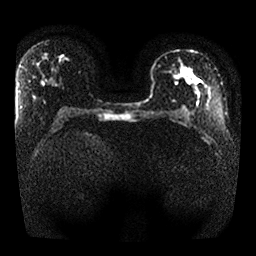
Breast MRI, one axial slice. Slice 13 of 25 in the series (ordered by position). Diffusion-weighted series; image 2 of 4 stored at this slice position (different b-values; order by instance number). 1.5 T. 4 mm slice thickness. 256 × 256 image matrix. Female patient.
Structures marked on this image (expert manual segmentation):
- tumour on diffusion-weighted imaging: bounding box (x1, y1, x2, y2) in pixels: (169, 69, 179, 80)